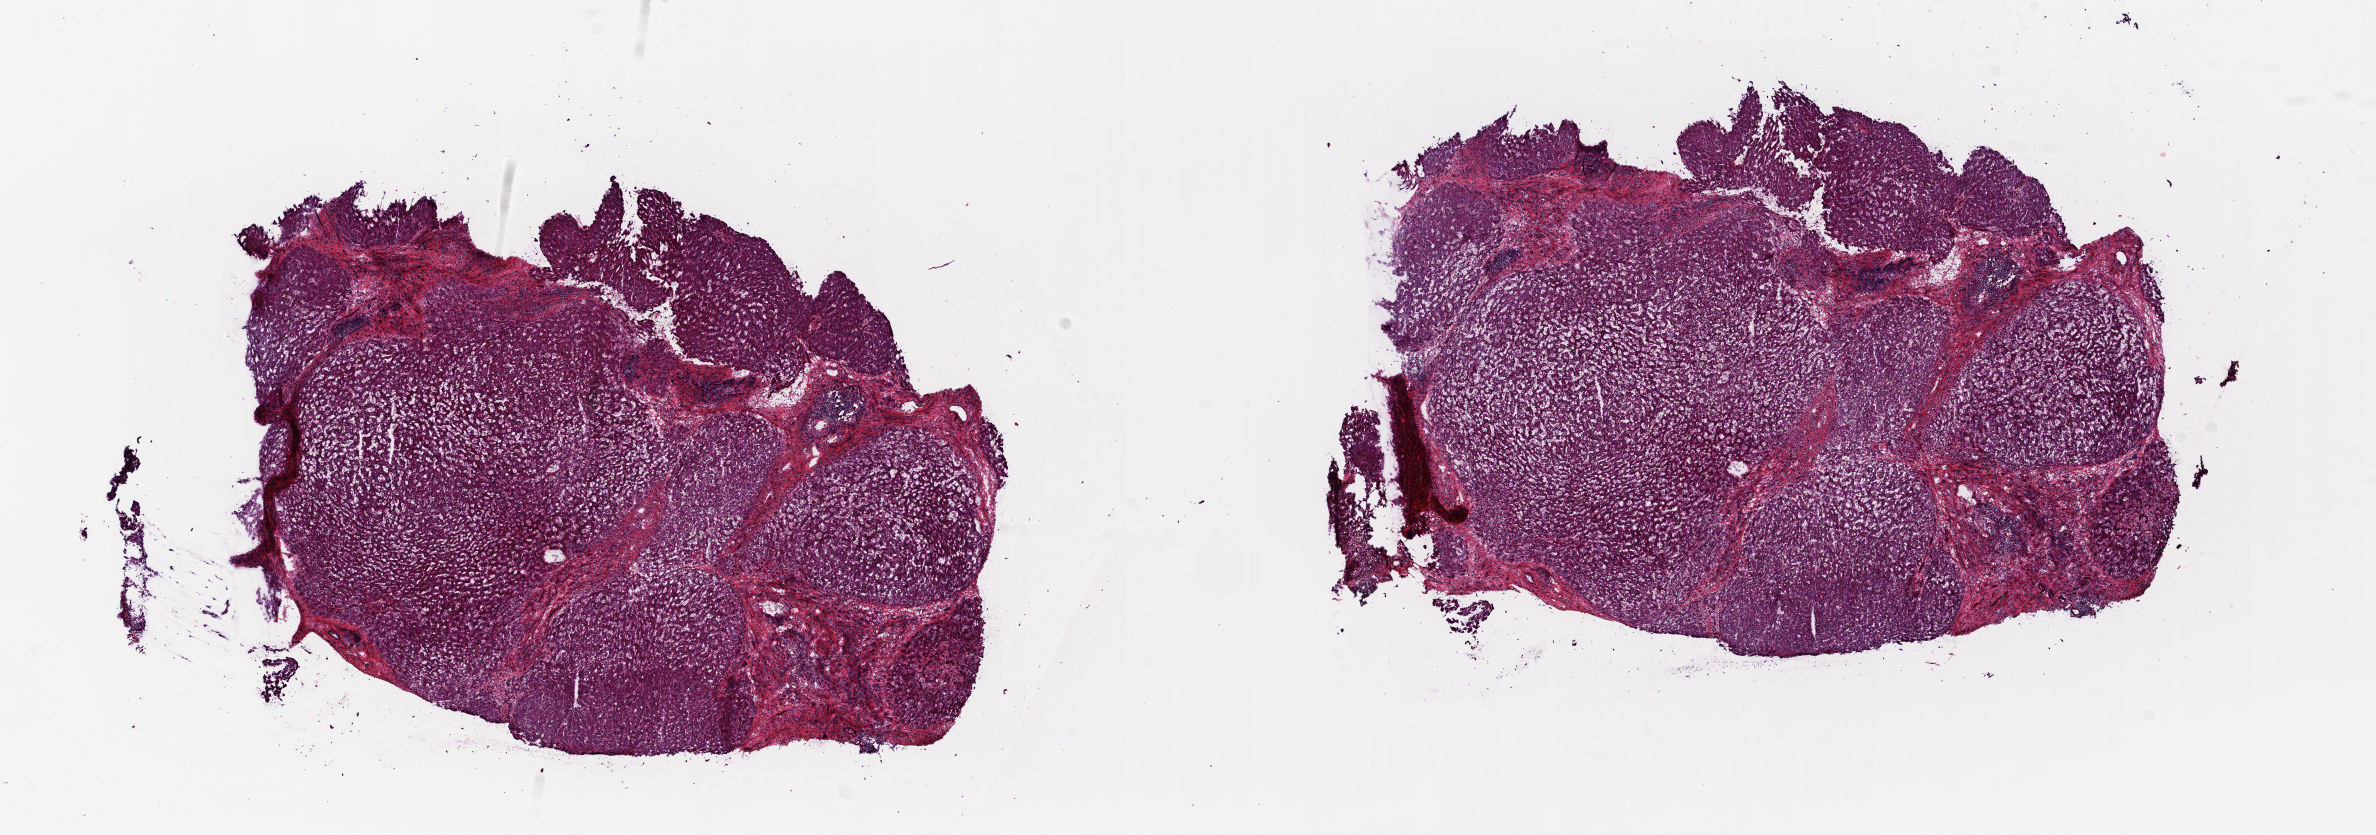
Whole-slide histology image, Hematoxylin and eosin (H&E) stained — shown as a low-resolution overview of the whole scanned area (about 18.8 x 6.6 mm), frozen section, solid tissue normal (non-tumour tissue) sample from the liver. Male patient; age at initial diagnosis 73 years. Slide review estimates, as recorded: tumour cells 0%, tumour nuclei 0%, normal cells 90%, stromal cells 10%, necrosis 0%. Infiltration values recorded for this section: lymphocyte infiltration 0%, monocyte infiltration 0%, neutrophil infiltration 0%.
This section: solid tissue normal sample (biorepository sample class). Patient diagnosis: Hepatocellular carcinoma, NOS.